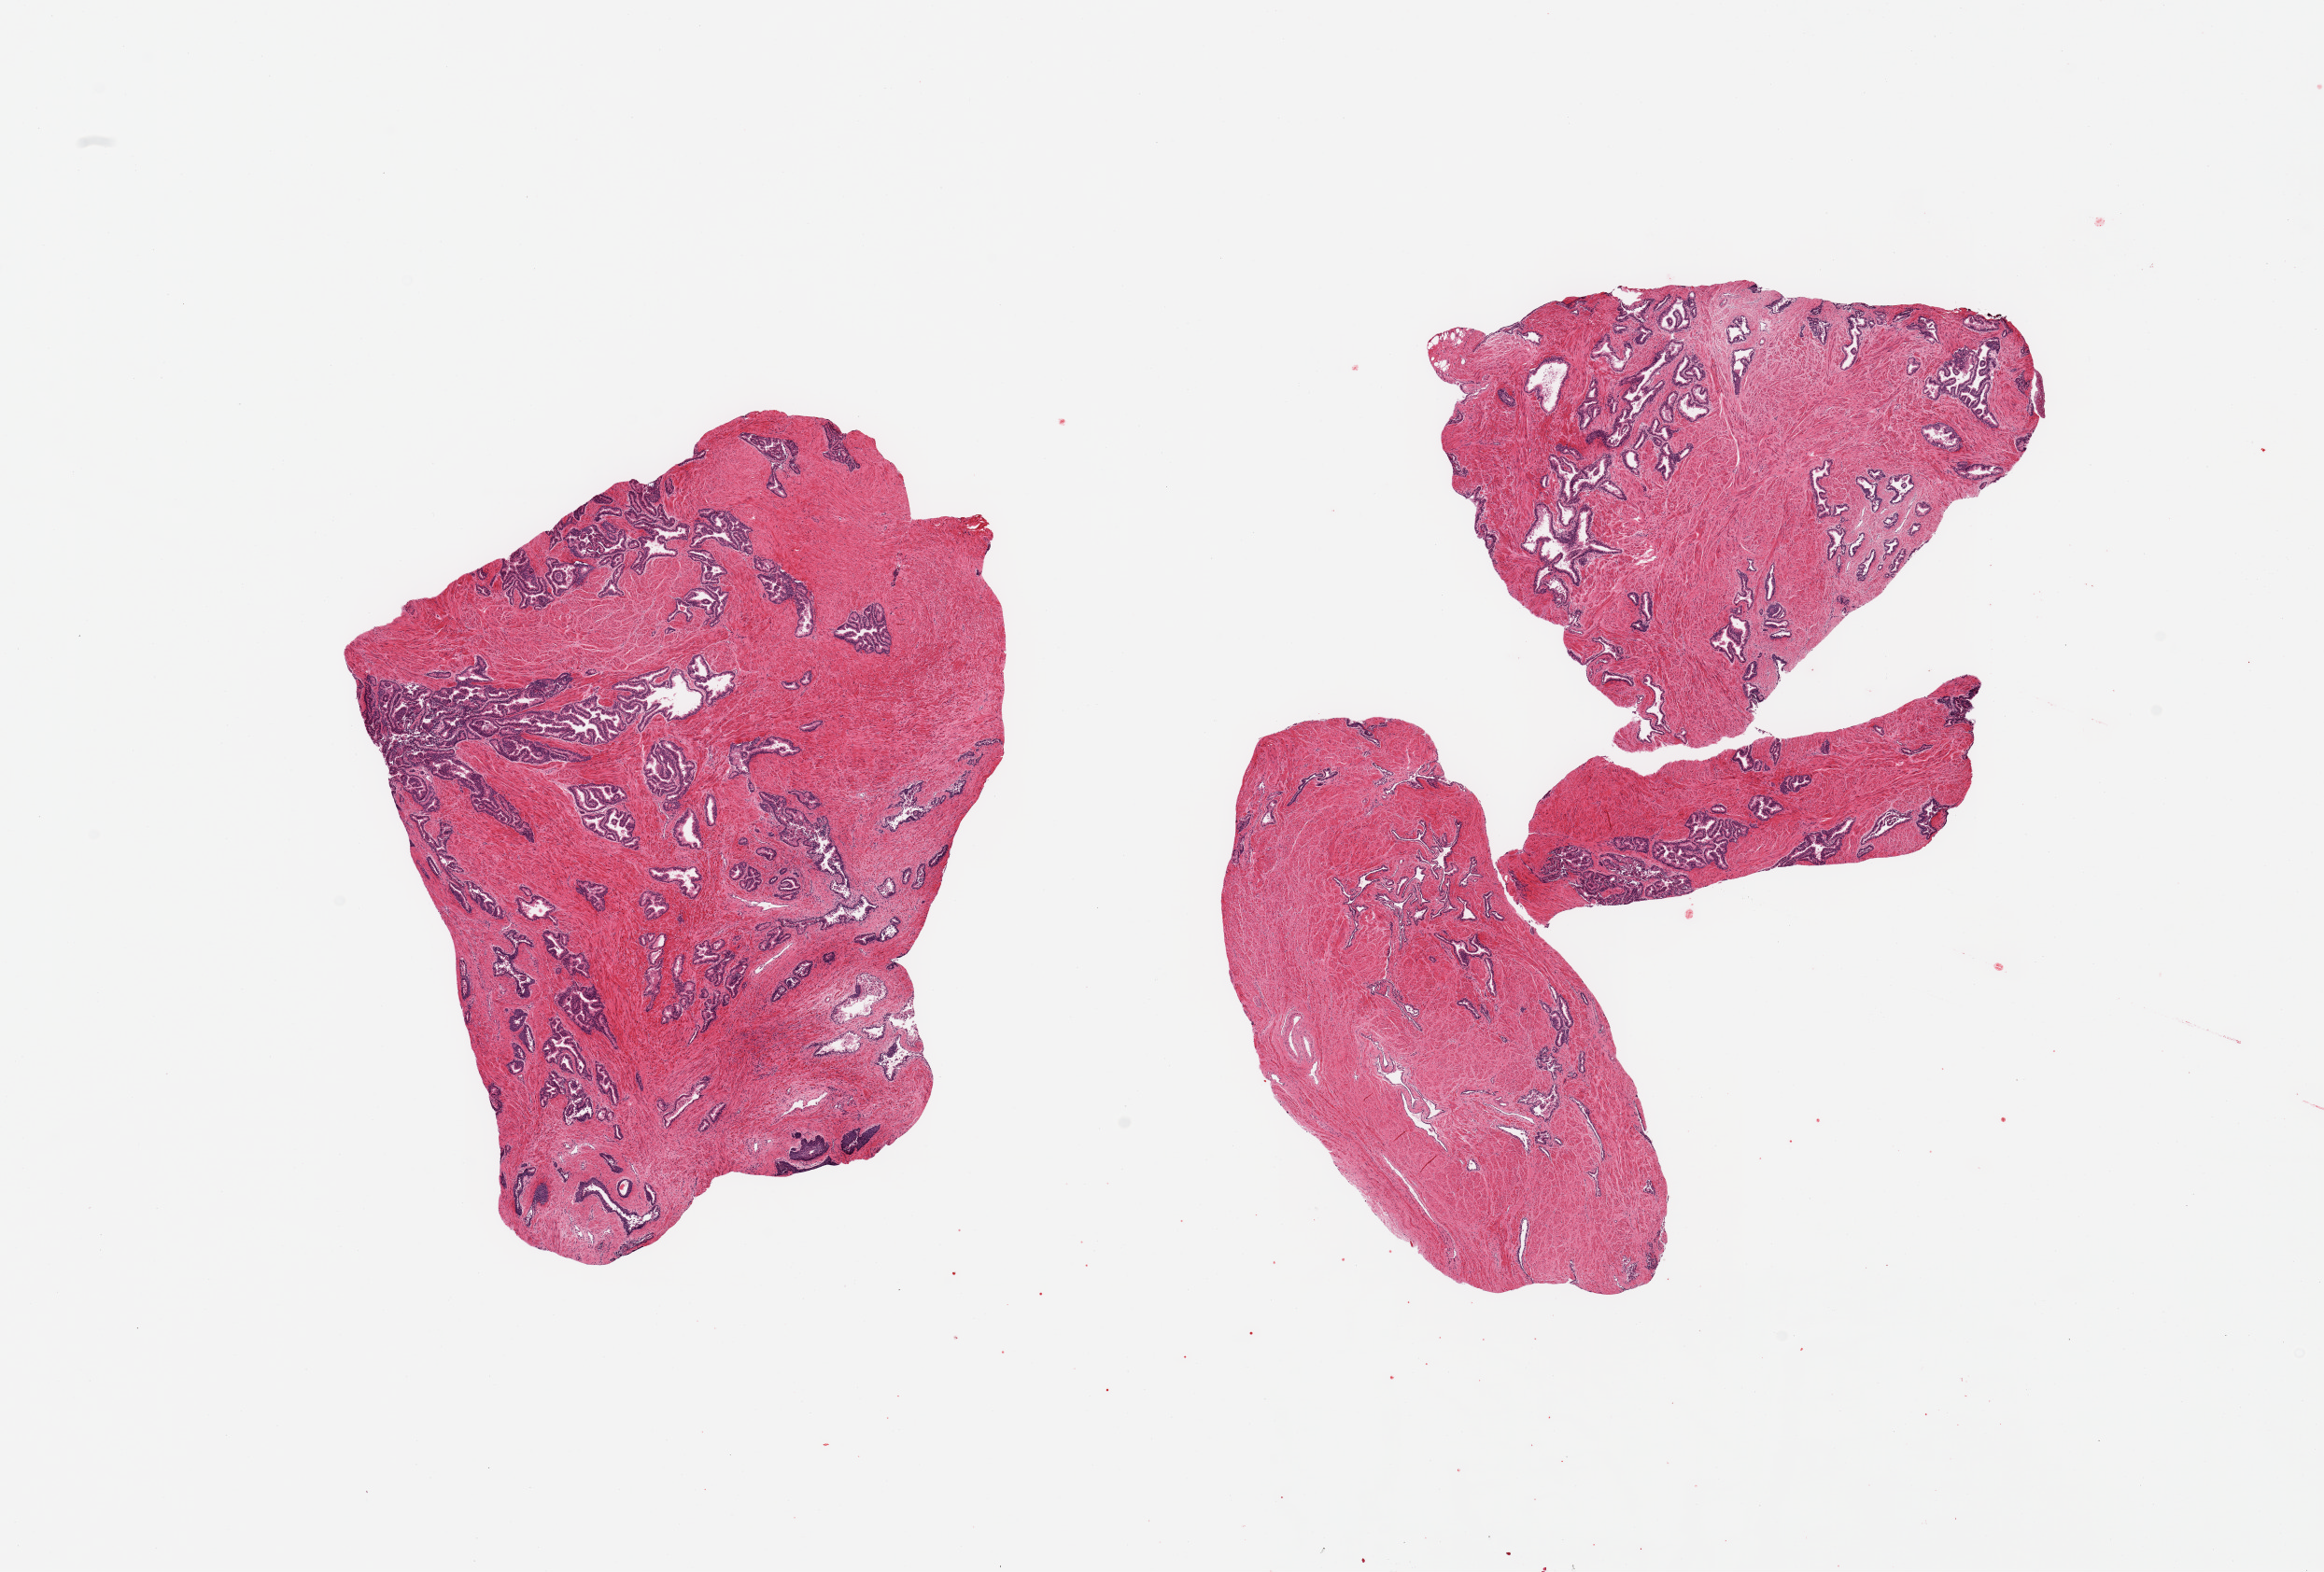
Digitized hematoxylin and eosin (H&E)-stained section — shown as a low-resolution overview of the whole scanned area (about 19.7 x 13.3 mm), PAXgene-fixed paraffin-embedded (PFPE) section, target tissue: prostate, tissue donor sample. Male donor.
• pathologist's review note for this sample: 4 pieces; well preserved glands